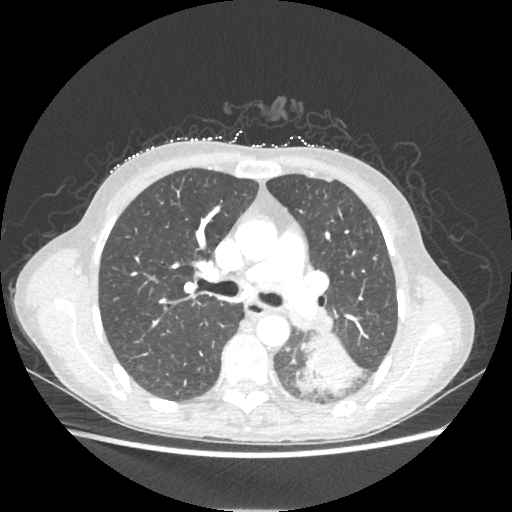
Chest CT, one axial slice. Slice 135 of 221 in the series (ordered by position). 80 kVp. Lung window (W 1500 / L -600 HU). 1.25 mm slice thickness. 512 × 512 image matrix, field of view 360 × 360 mm. Patient: female, 53 years. Case-level facts recorded for this patient, not image findings: clinical TNM (as recorded): T3 N0 M0.
Structures marked on this image (bounding box drawn by a radiologist):
- lung tumour (recorded histology: adenocarcinoma): bounding box <297,332,362,394> (left, top, right, bottom; pixels)